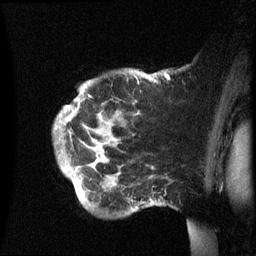
Breast MRI (dynamic contrast-enhanced), one sagittal slice; position 48 of 60 along the scan axis; dynamic contrast-enhanced series, image 2 of 3 at this slice position (ordered by acquisition); 1.5 T; TE 4.2 ms, TR 8.4 ms; 256 × 256 image matrix, field of view 230 × 230 mm. Patient: female, 49 years.
Outlined on this slice (semi-automatic segmentation, software-assisted and operator-edited):
- analysis volume of interest (the breast-tissue region the enhancement analysis was run in; not a lesion): box from (x=54, y=69) to (x=166, y=216) px
- tumour enhancement mask (voxels above the 70 % enhancement threshold inside the analysis volume of interest): (x=66, y=106)–(x=110, y=187)